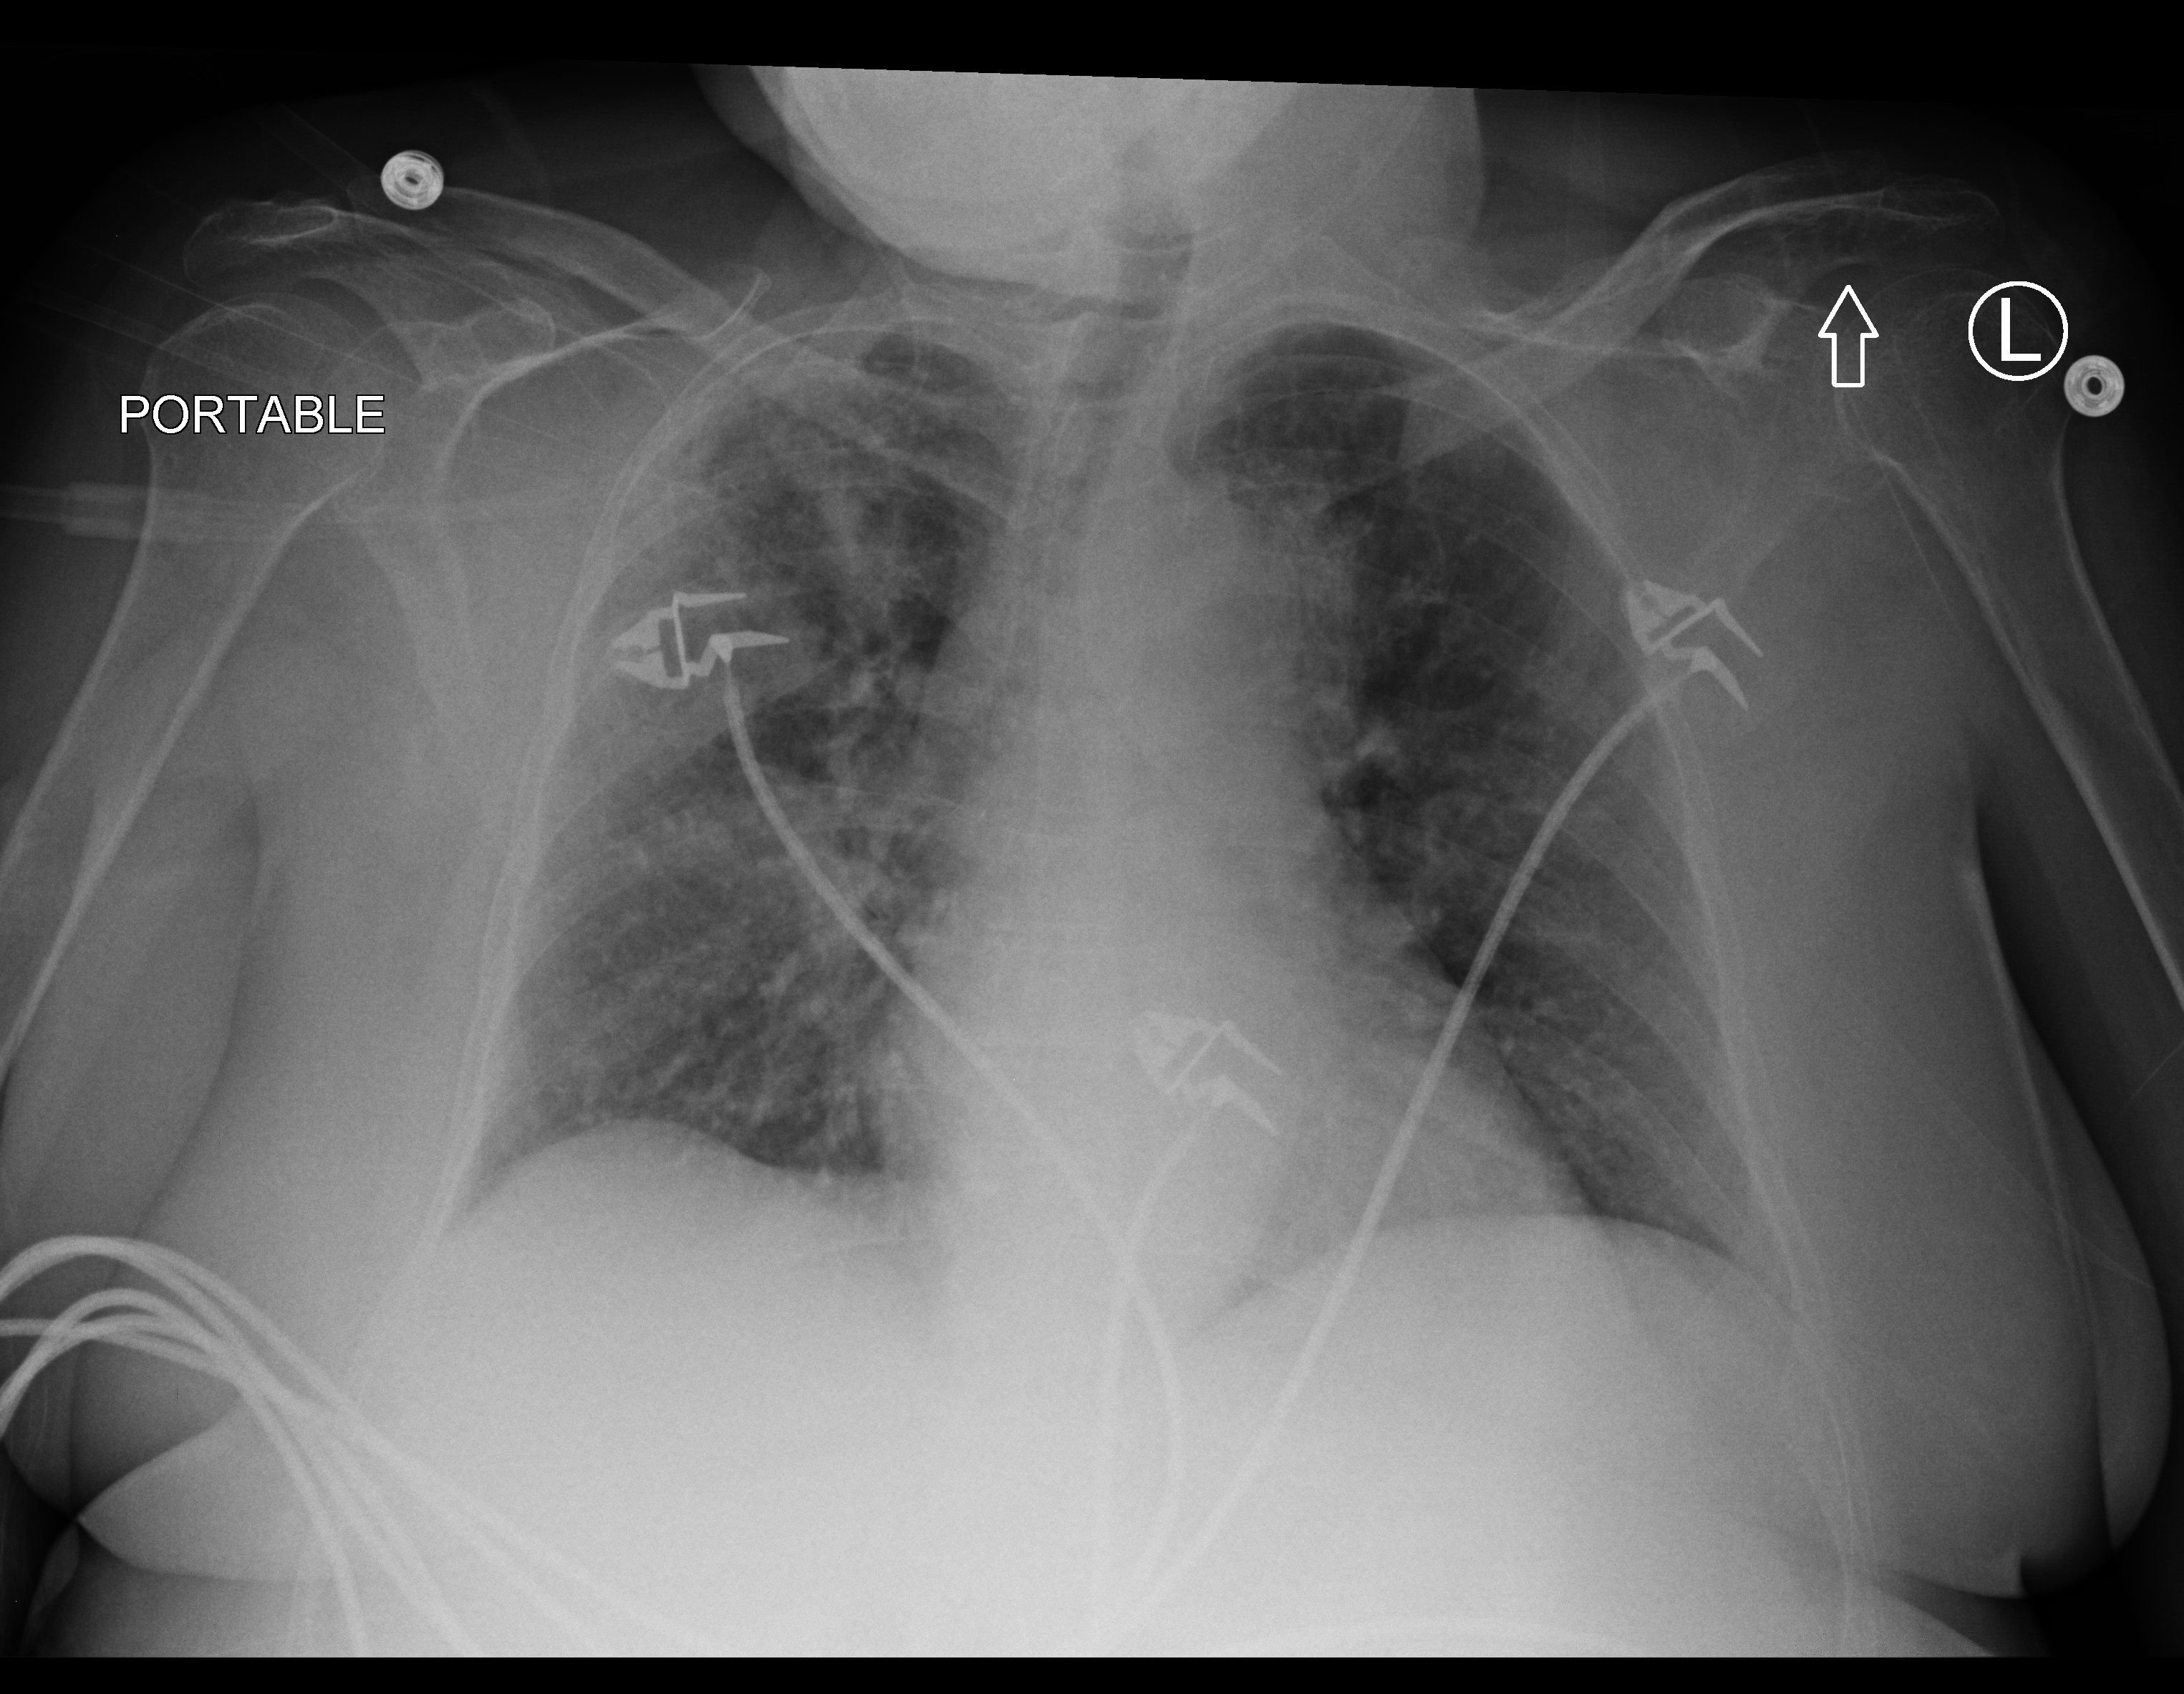
Portable chest radiograph. Patient hospitalised with COVID-19; female, aged 18–59 years.
Admission-level facts for this patient (not findings on this image; timing relative to this image not recorded): mechanically ventilated during this hospital stay: no; admitted to intensive care during this hospital stay: no.